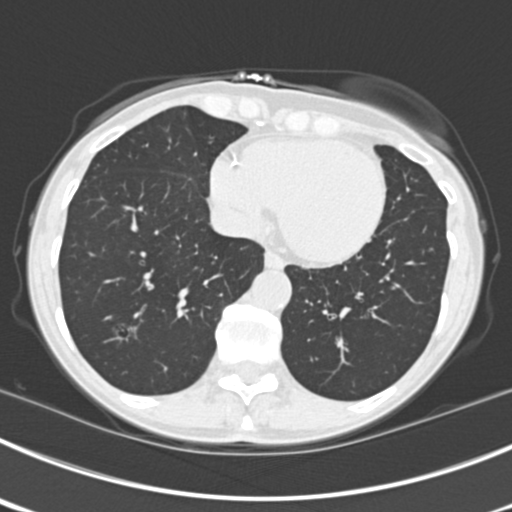
Axial slice from a low-dose chest CT screening exam, third screening round (two years after baseline), lung window (W 1500 / L -600 HU), standard (soft-tissue) reconstruction kernel (B30f). Female, age 63 years at enrolment. Current smoker at enrolment.
Expert-annotated lung lesion, bounding box (x1, y1, x2, y2) in pixels: (103, 311, 148, 358). The screening reader recorded 9 non-calcified nodules or masses ≥4 mm on this exam (left upper lobe, right upper lobe, left upper lobe, left lower lobe, right middle lobe, left lower lobe, left lower lobe, right lower lobe, right lower lobe); which of them this box marks is not recorded. Lung cancer was diagnosed 15 days after this screen: bronchiolo-alveolar adenocarcinoma, NOS, right upper lobe, right middle lobe, right lower lobe, left upper lobe, left lower lobe, moderately differentiated (G2), stage IV (AJCC 6th edition).